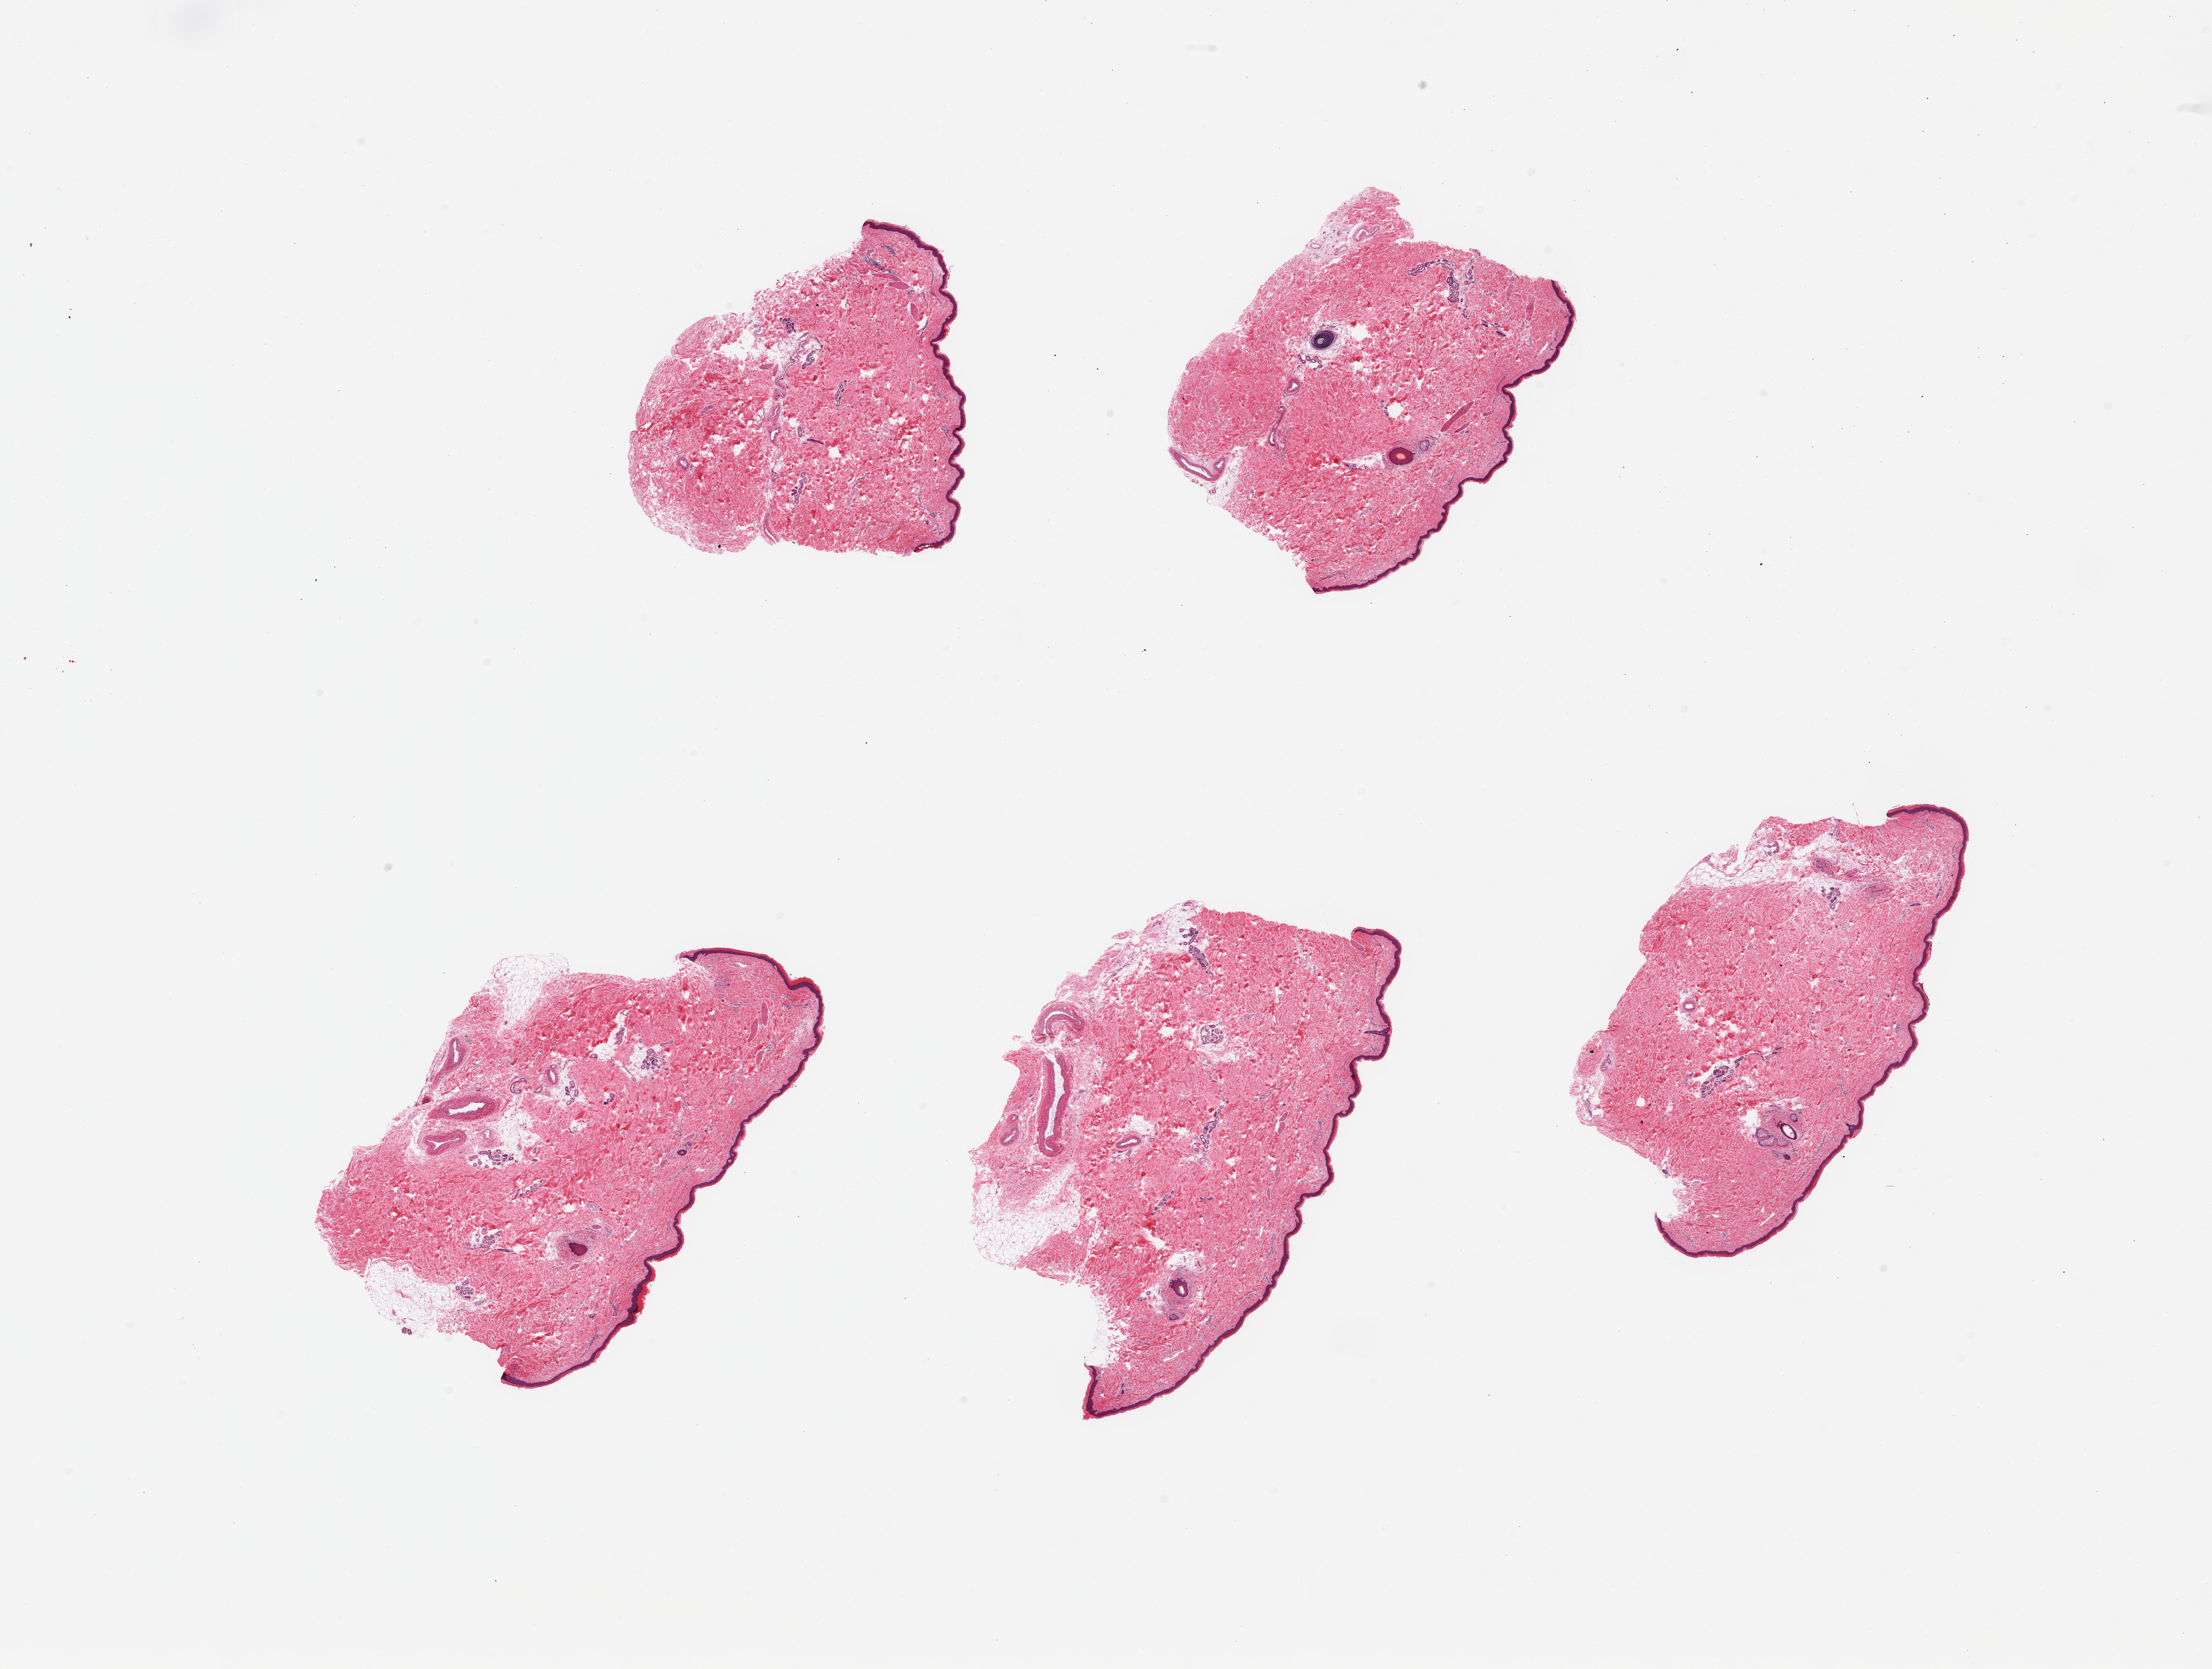
Digitized H&E-stained section, whole scanned area (about 27.6 x 20.8 mm) shown as a low-resolution overview. PAXgene-fixed paraffin-embedded (PFPE) section. Sampled site (target tissue): skin of lower leg. Donor tissue sample. Male donor.
- pathologist's review note for this sample: 6 pieces; trace periadnexal fat; epidermis 36 micron thick; rare hair follicles